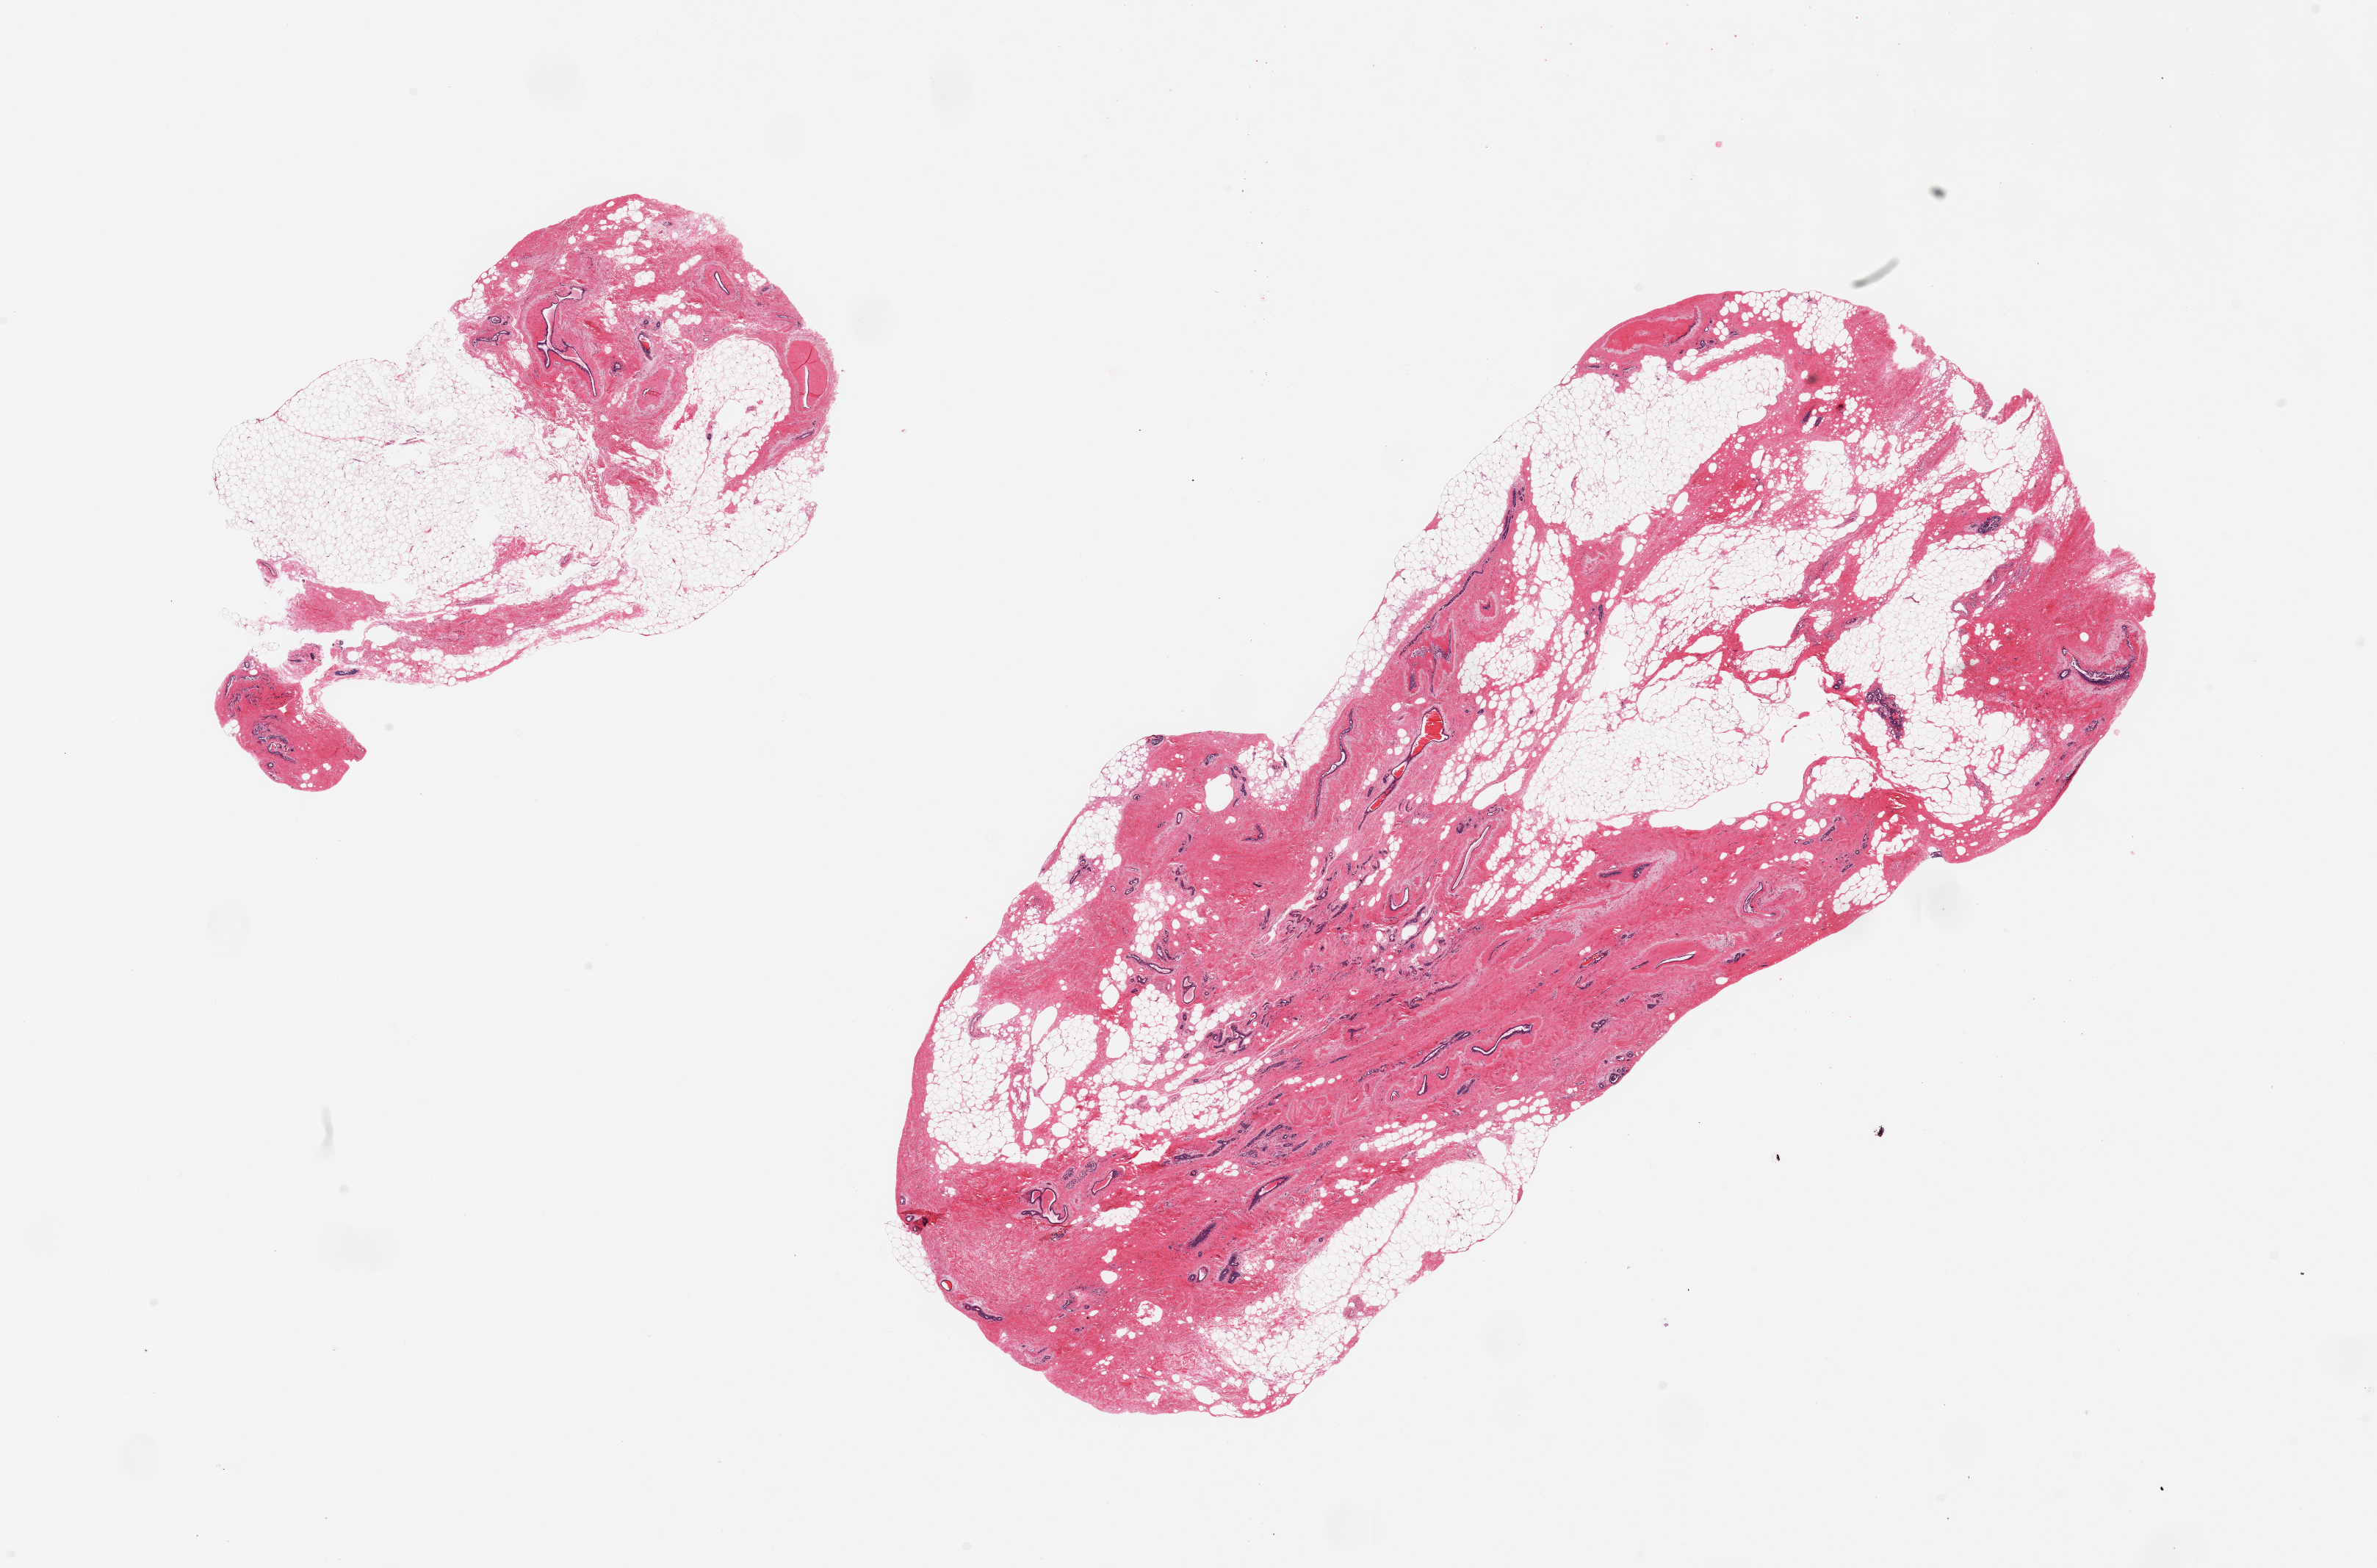
Whole-slide image, H&E stain, whole scanned area (about 25.6 x 16.9 mm) shown as a low-resolution overview, PAXgene-fixed, paraffin-embedded tissue, section of breast (target tissue), donor tissue sample. Donor: female.
Reviewer comment on this tissue sample: 2 pieces; fat with dense fibrocollagenous stroma with interspersed benign ductal/lobular elements.